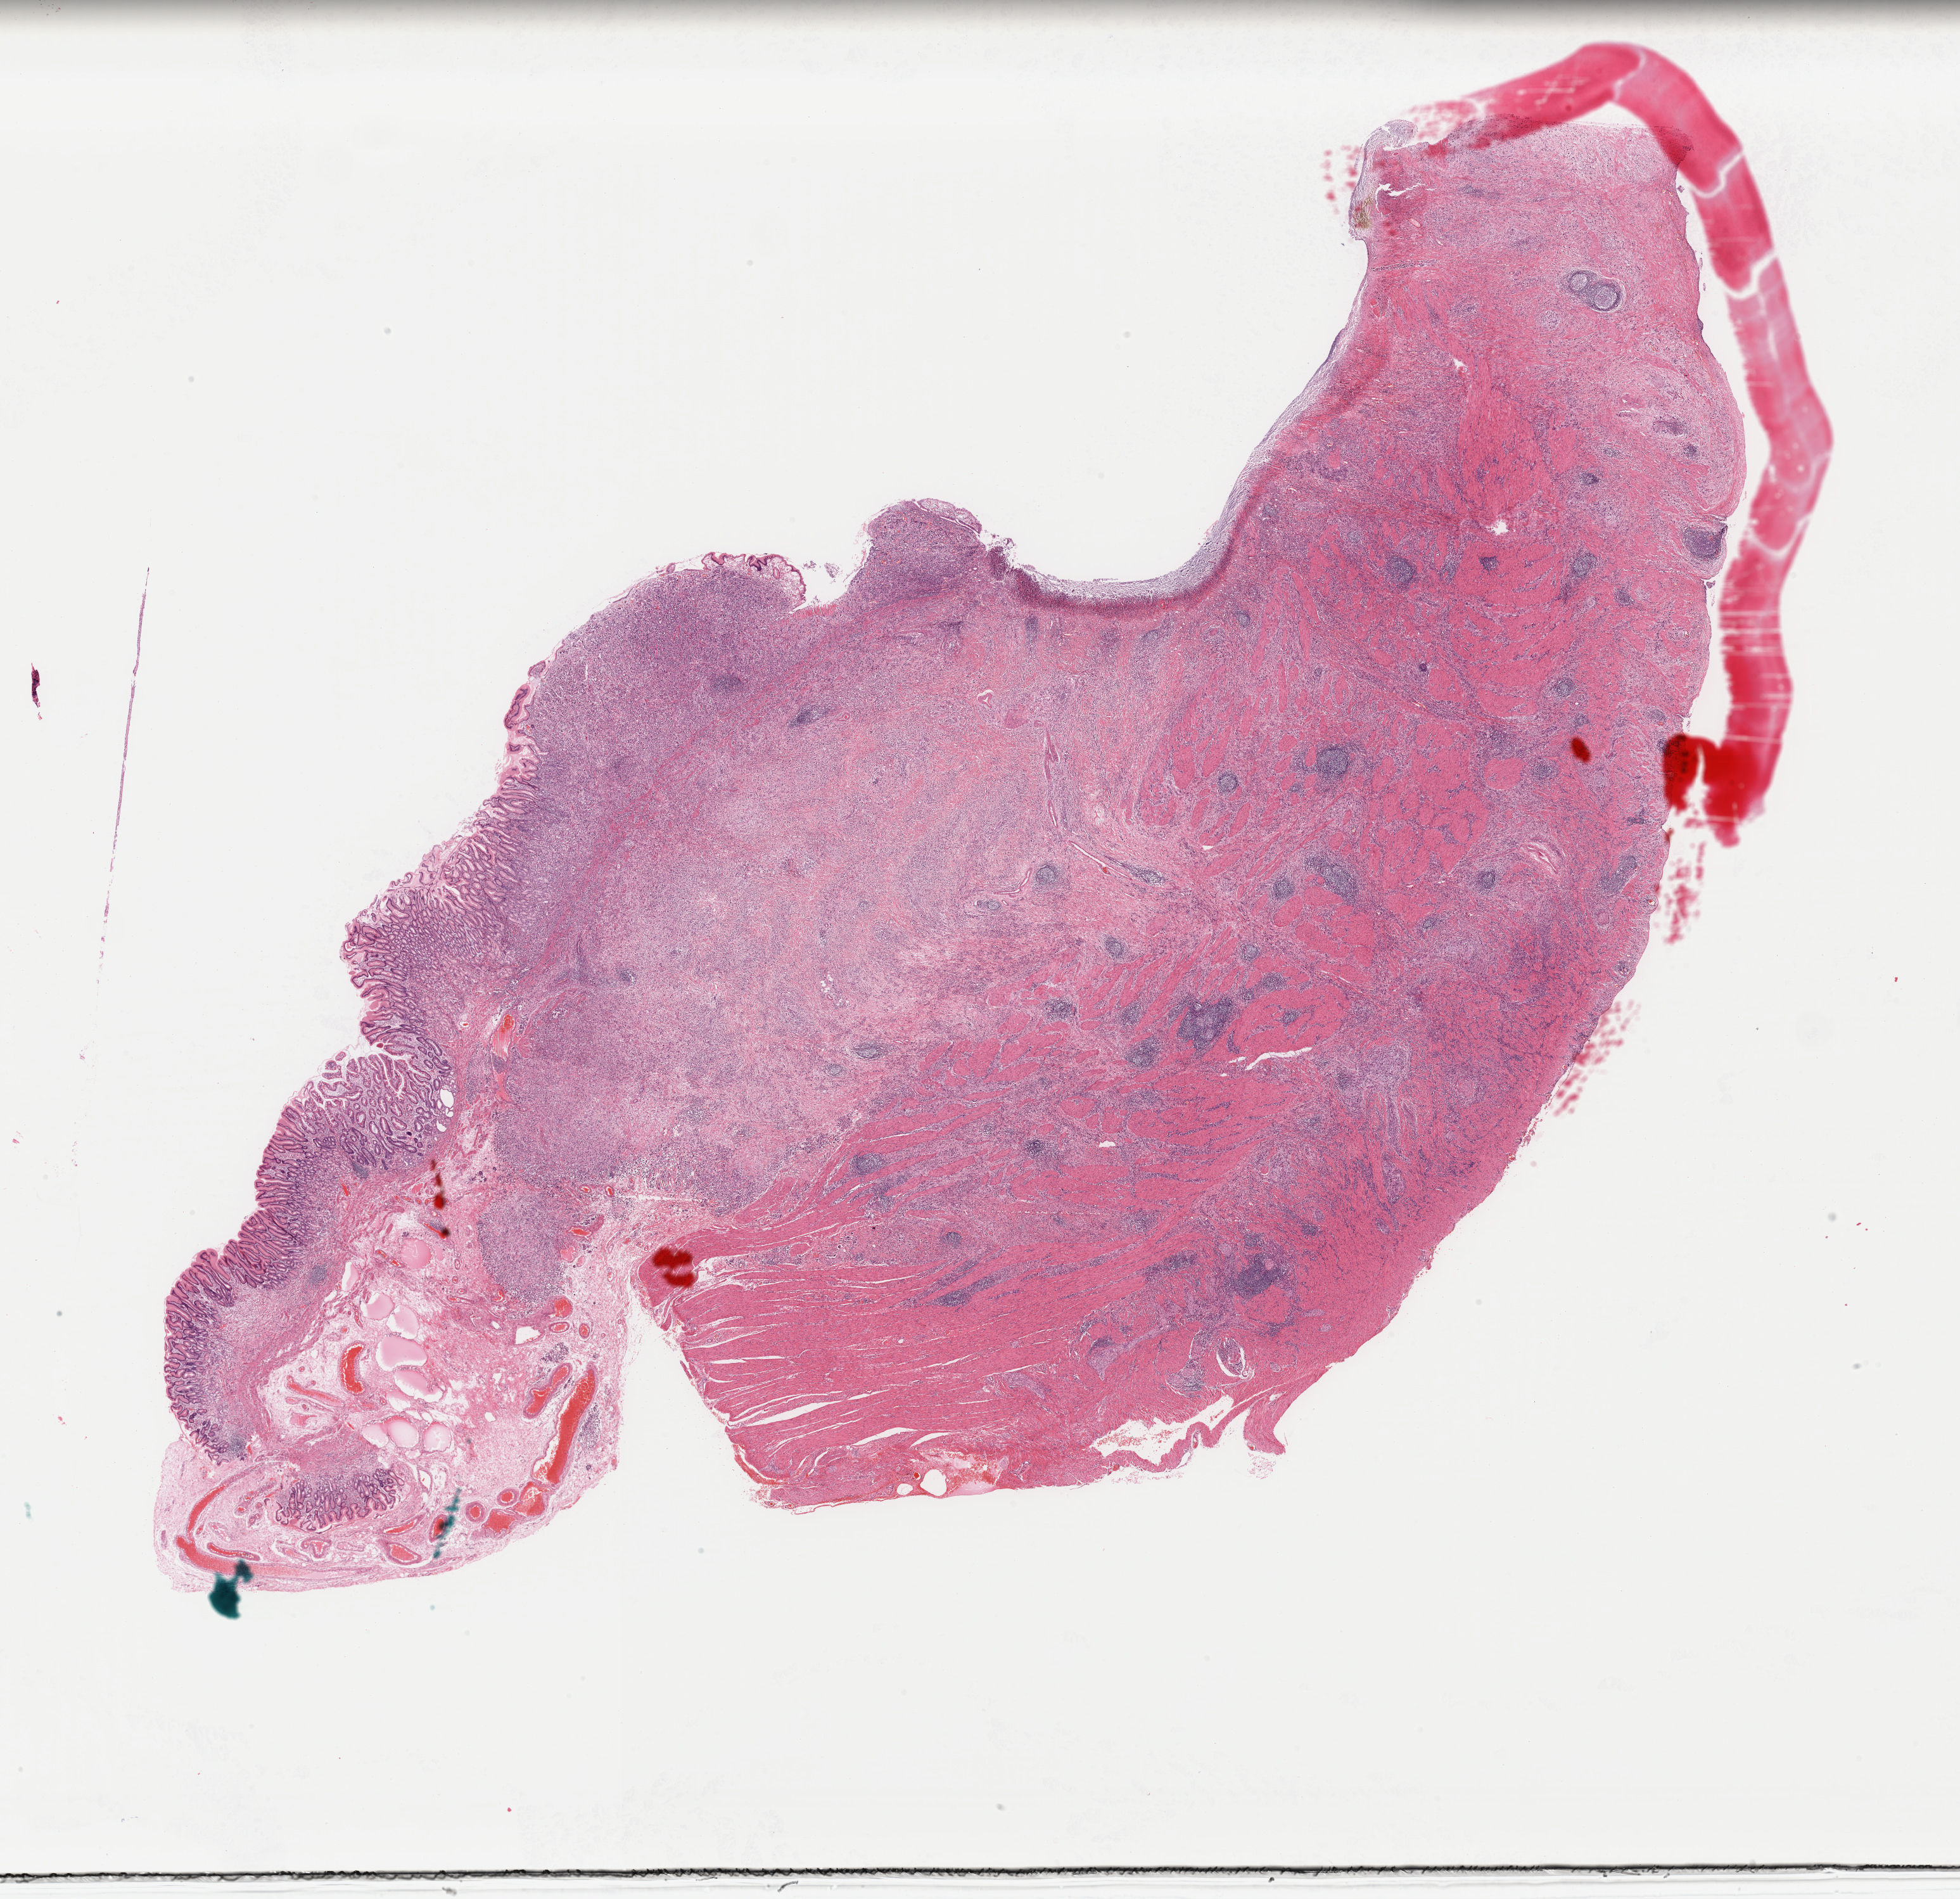
Whole-slide histology image, Hematoxylin and eosin (H&E) stained, low-resolution overview of the scanned area, about 24.4 x 23.7 mm. FFPE section. Primary tumour sample from the stomach. Patient: male, age at initial diagnosis 70 years. Histologic grade: G3 (poorly differentiated).
• AJCC pathologic stage: IIB
• pathologic diagnosis: Carcinoma, diffuse type
• TNM: T4a N0 M0